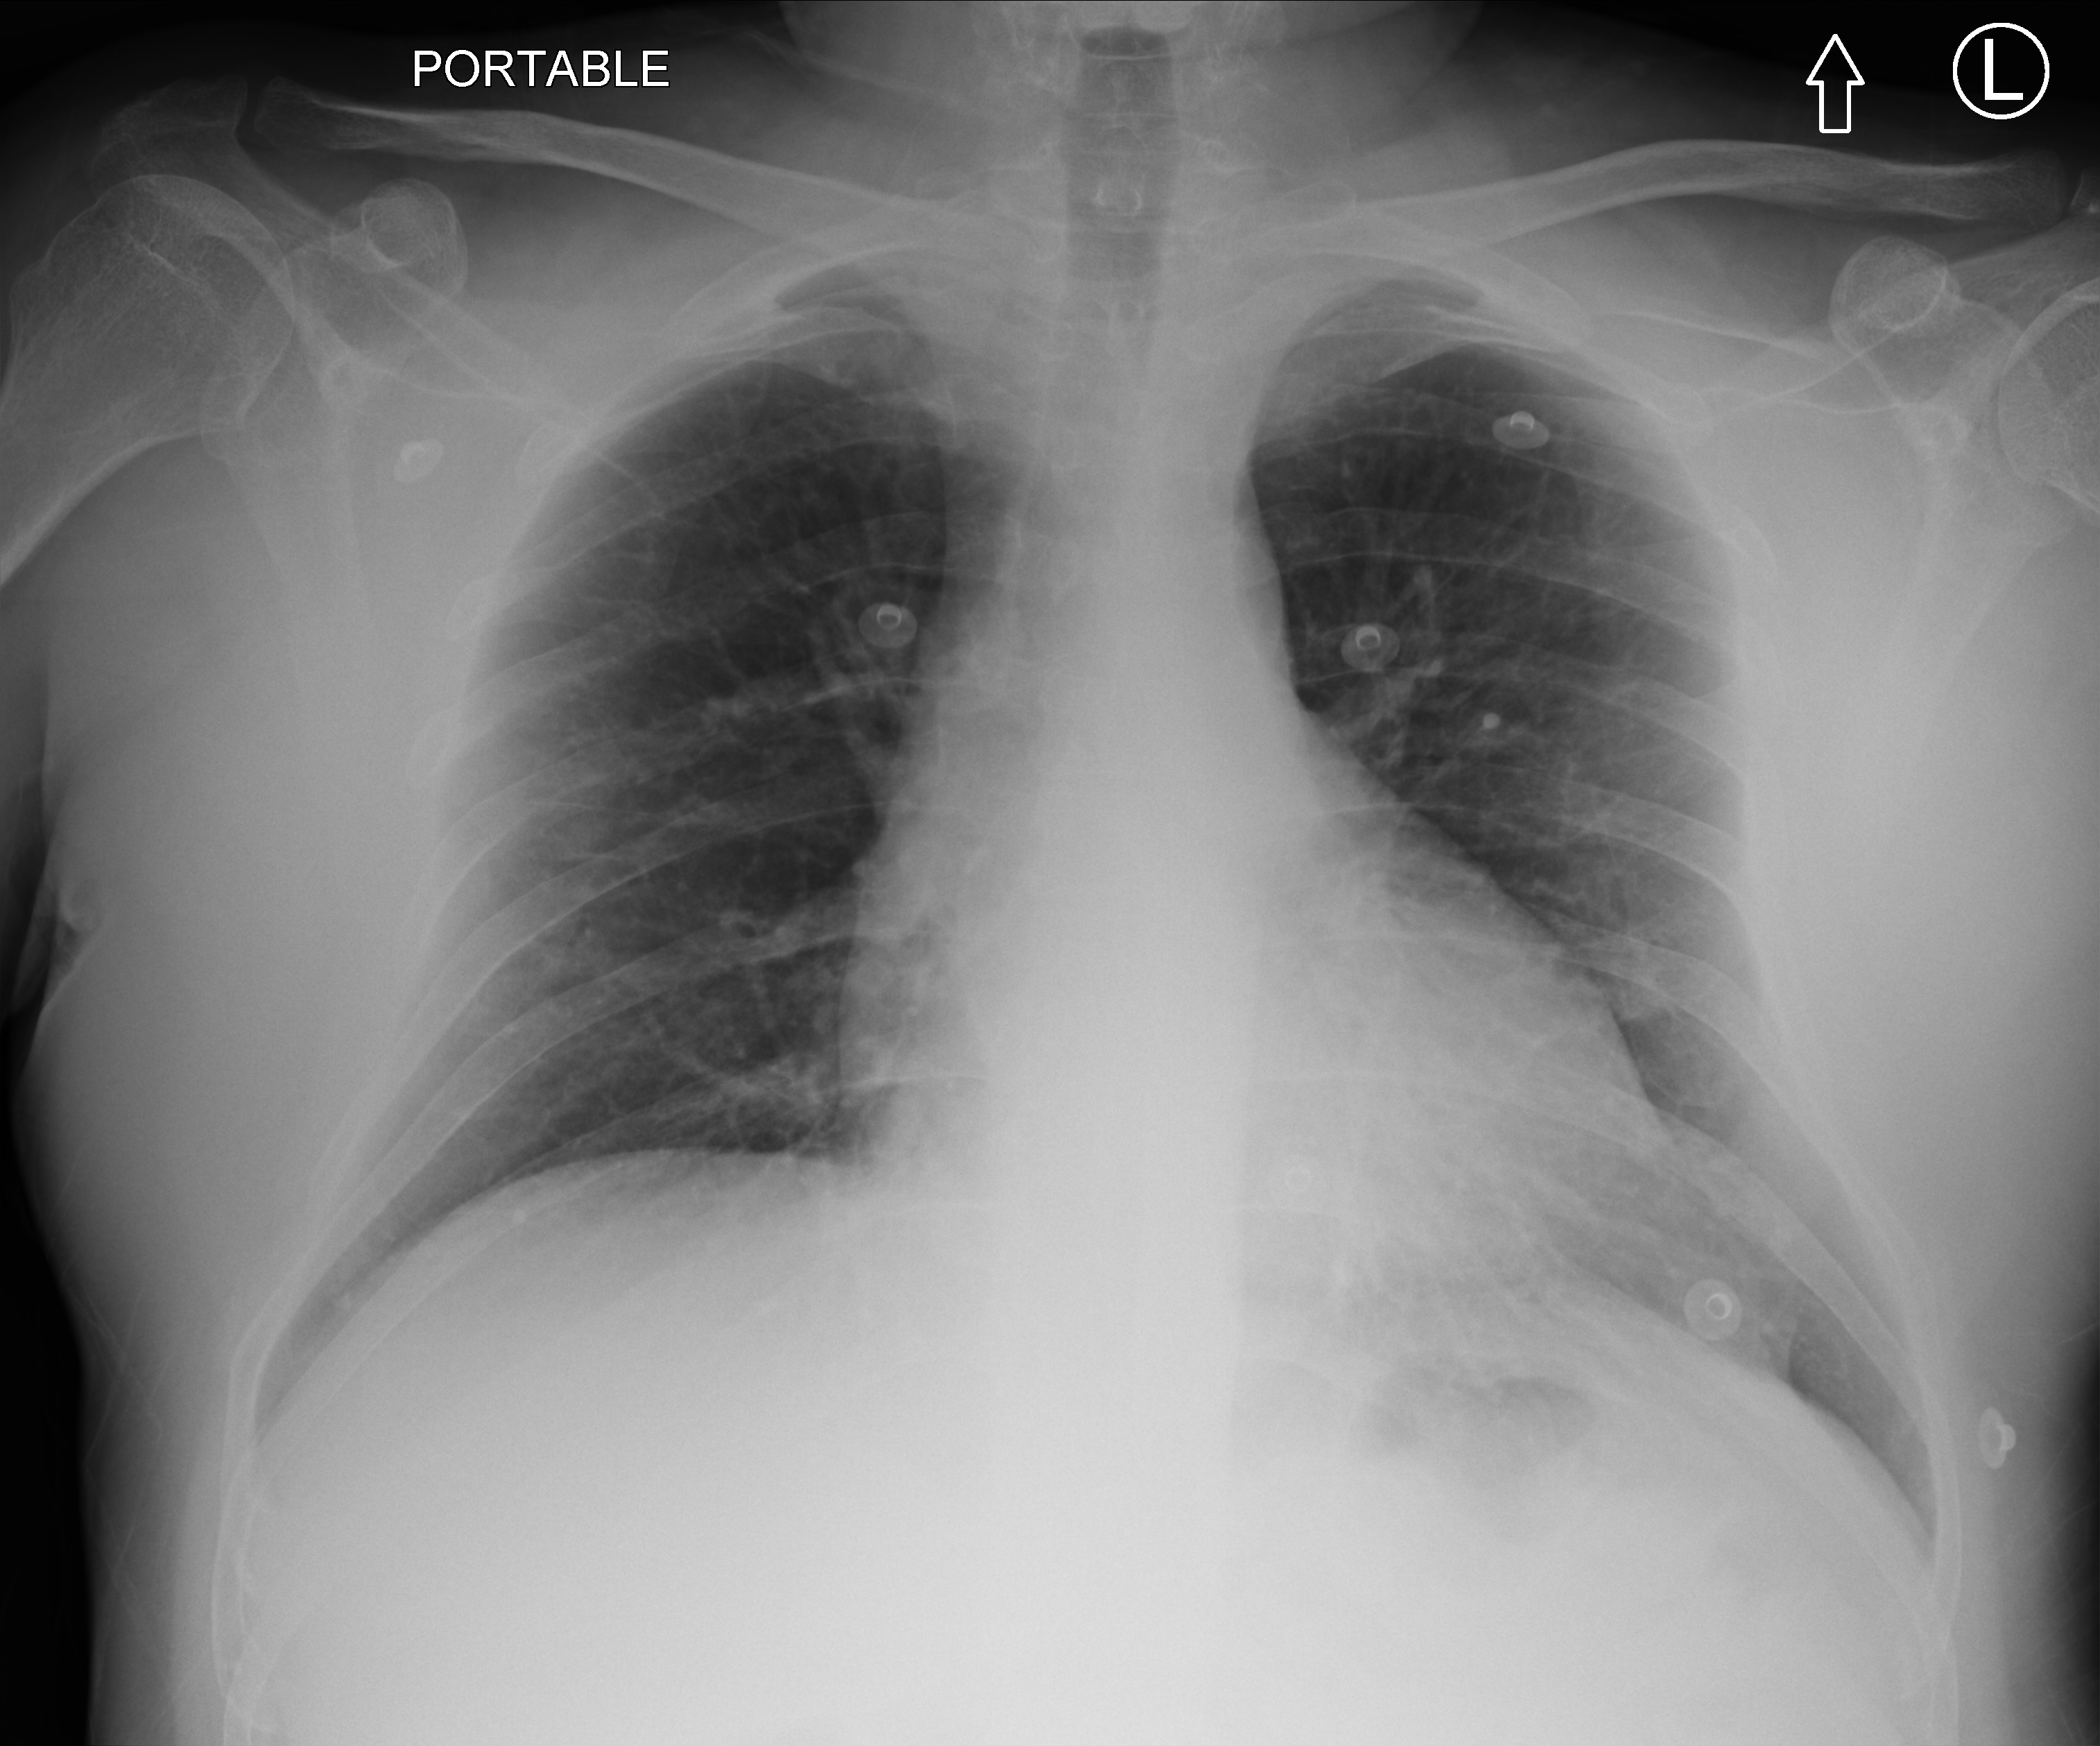
Bedside chest radiograph (computed radiography). Patient hospitalised with COVID-19; male, aged 18–59 years.
From the hospital-stay record, not from the radiograph (when in the stay this image was taken is not recorded):
- length of hospital stay: 2 days
- admitted to intensive care during this hospital stay: no
- mechanically ventilated during this hospital stay: no